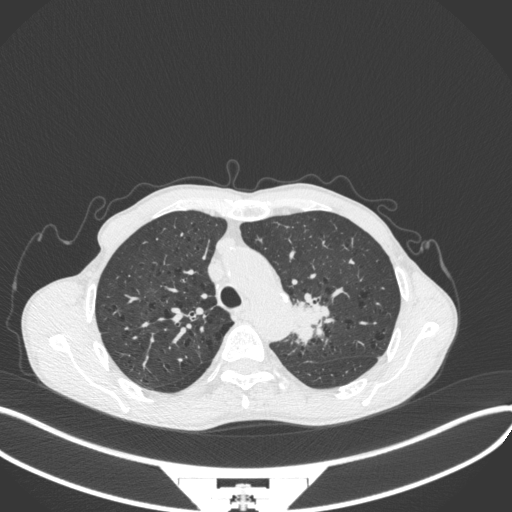
Chest CT, one axial slice. Reconstruction kernel B31f. 120 kVp. Lung window (W 1500 / L -600 HU). 1 mm slice thickness. 512 × 512 image matrix, field of view 400 × 400 mm. Male patient, age 65 years. From the clinical record (not read from this slice): clinical TNM (as recorded): T2b N0 M0; histopathological grade: G2.
Structures marked on this image (rectangle marked by the reading radiologist):
- lung tumour (recorded histology: adenocarcinoma): bounding box <287,292,332,346> (left, top, right, bottom; pixels)